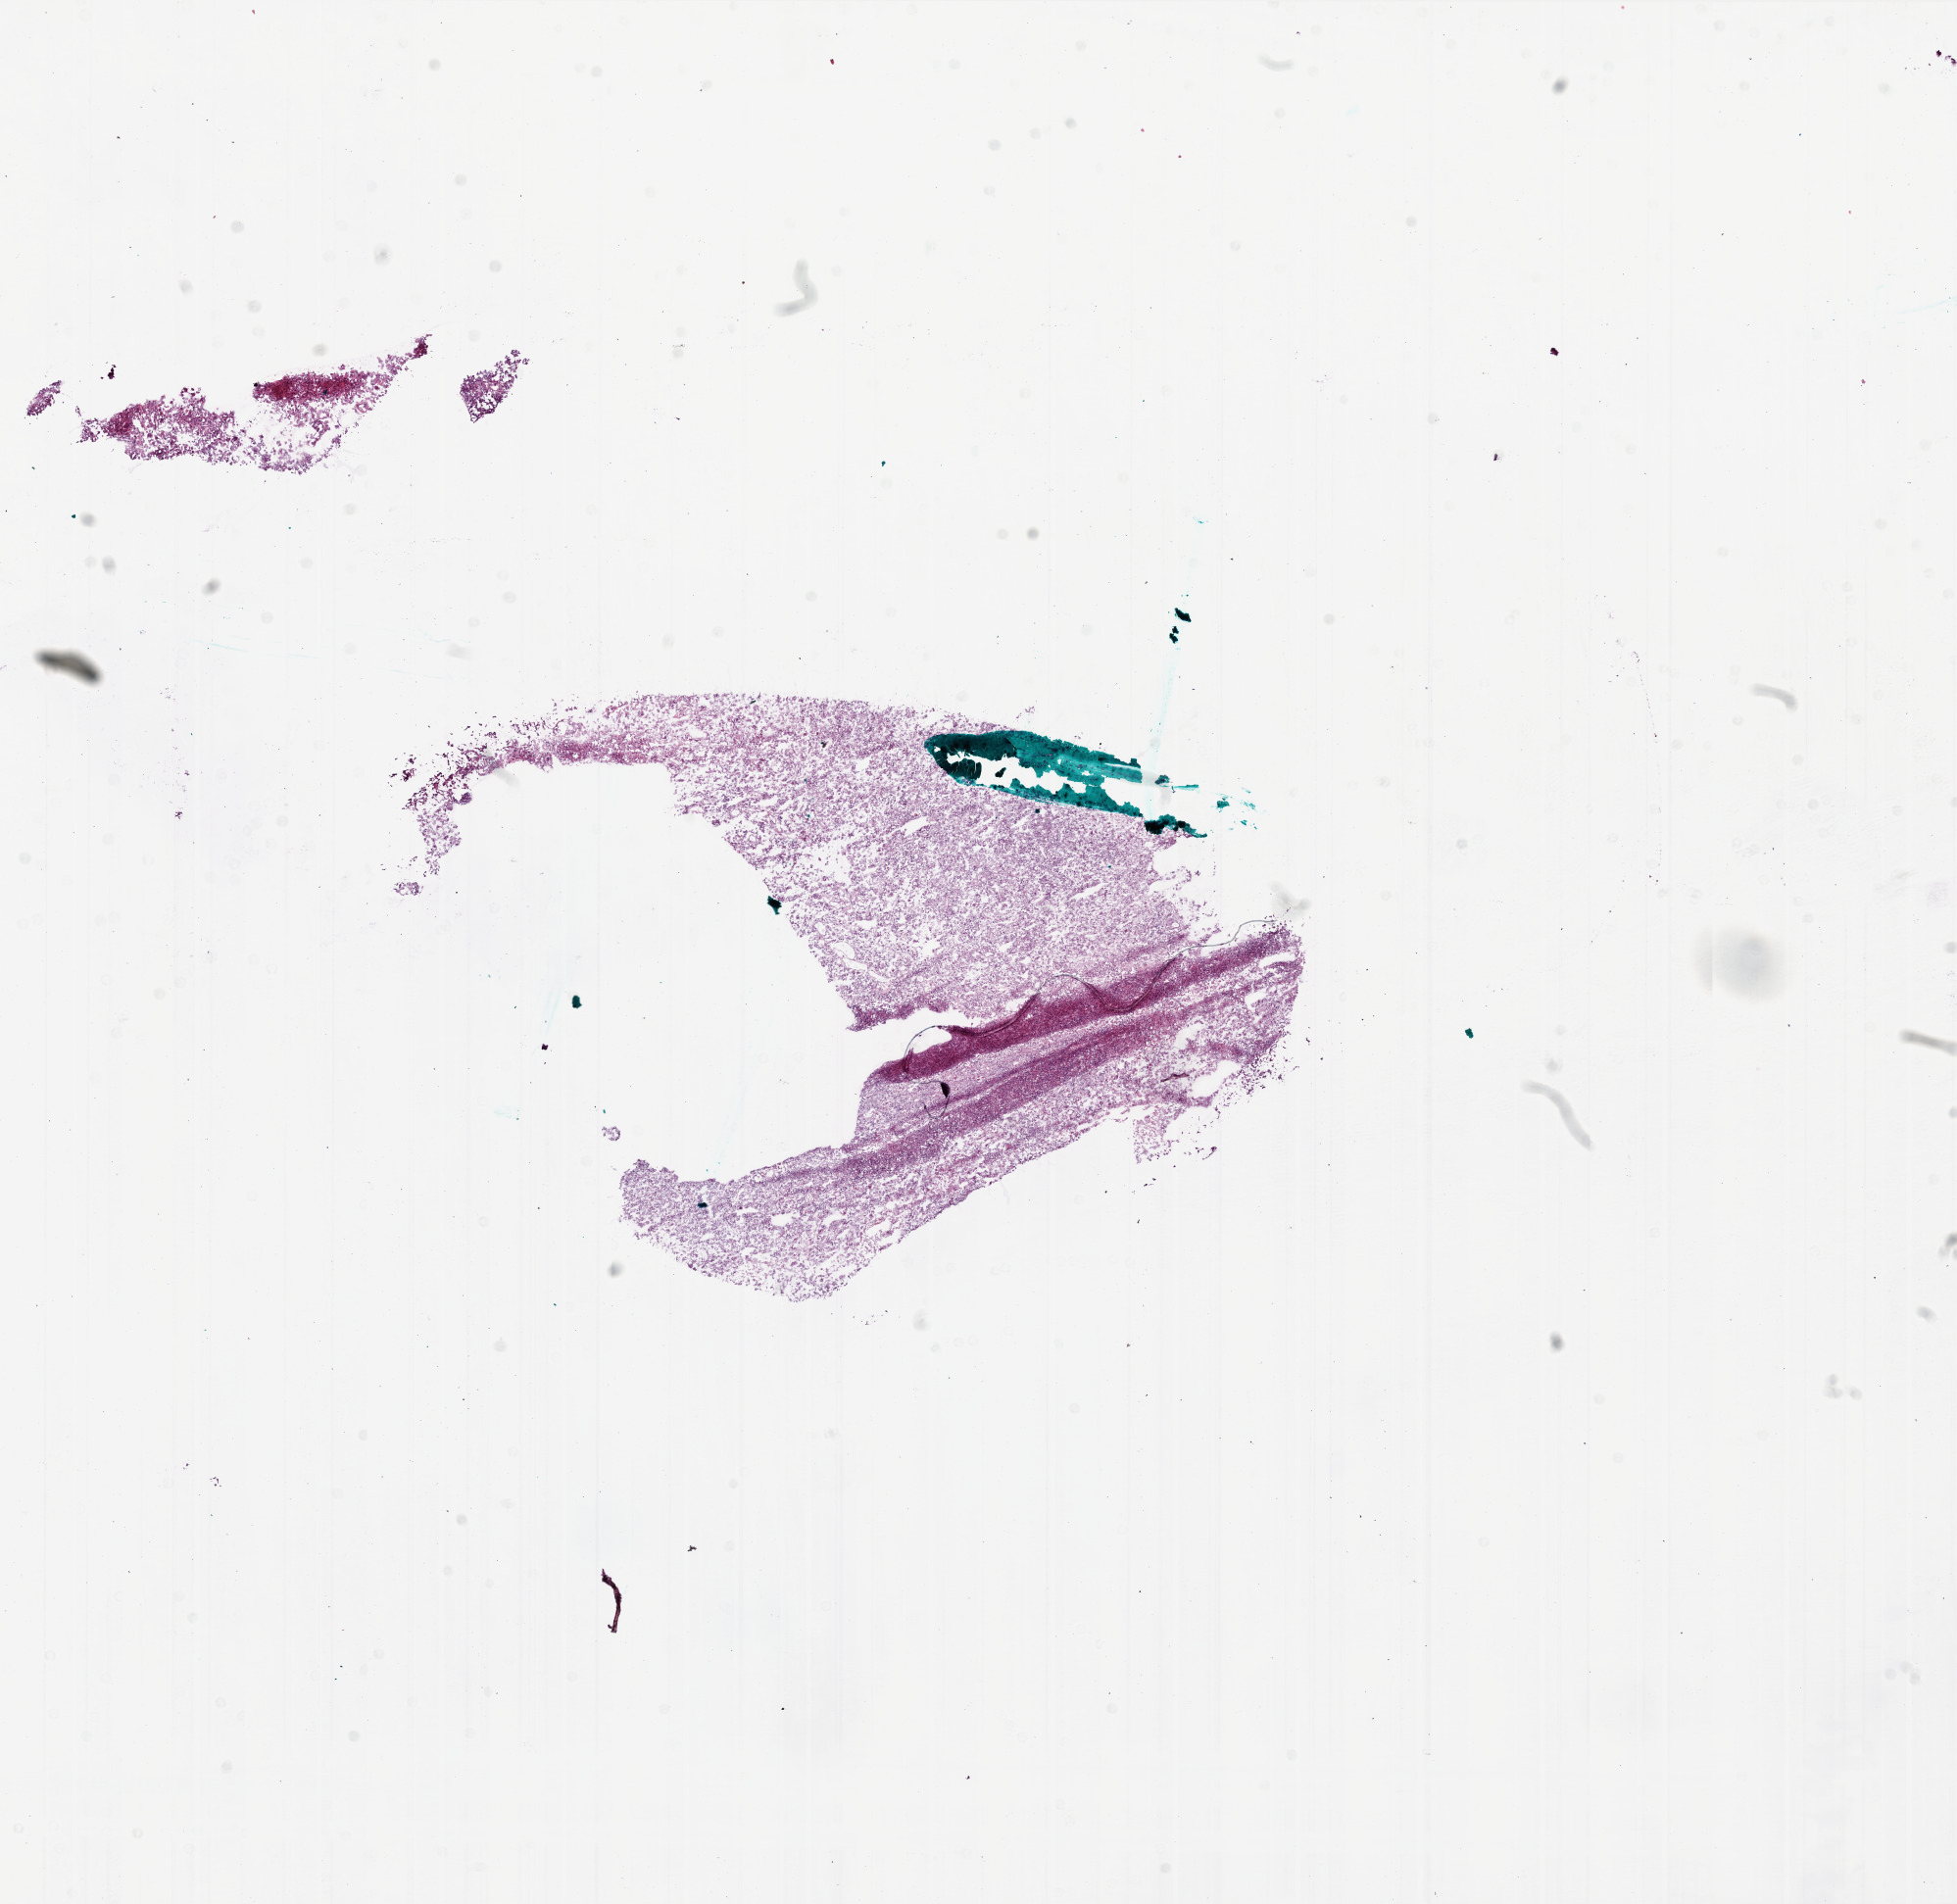
Whole-slide histology image, Hematoxylin and eosin (H&E) stained — a low-resolution overview of the entire scanned area, about 16.0 x 15.6 mm. Frozen section from the bottom of the tissue portion. Brain, primary tumour sample. Female, age 34 years at initial diagnosis. Slide review estimates, as recorded: tumour cells 100%, tumour nuclei 100%, normal cells 0%, stromal cells 0%, necrosis 0%.
- diagnosis: Glioblastoma